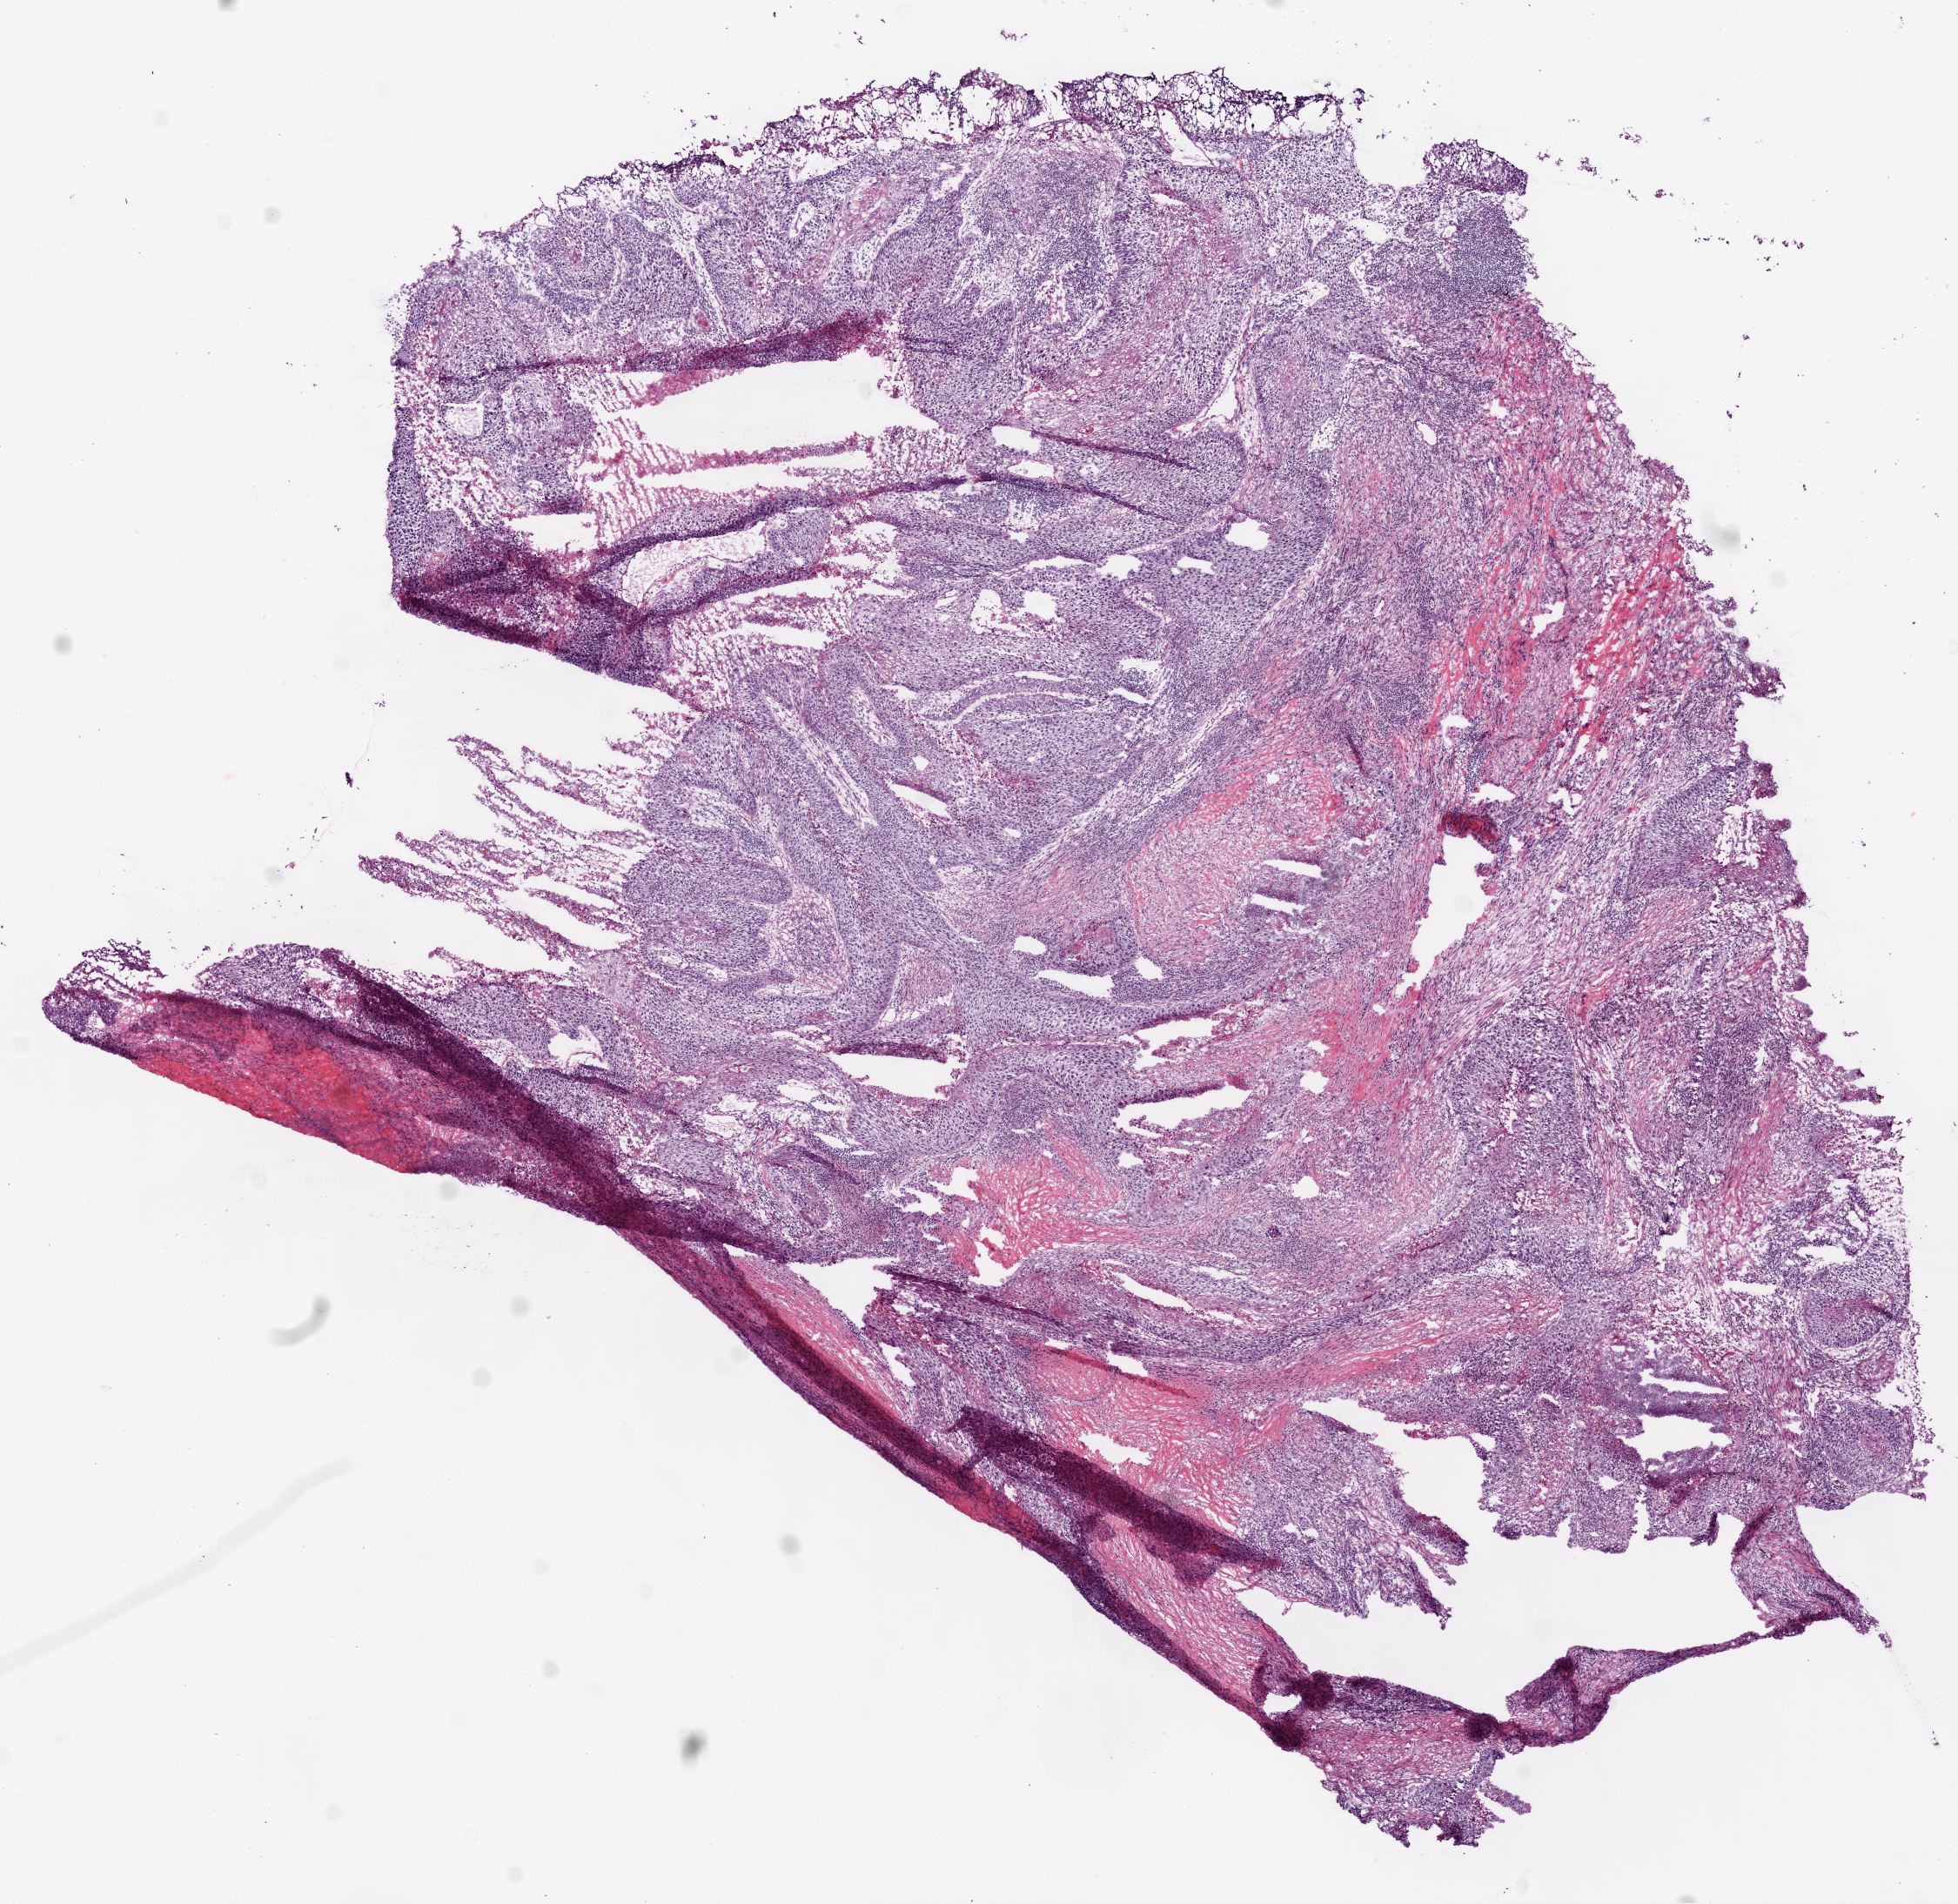
Whole-slide histology image, H&E-stained — whole scanned area (about 9.0 x 8.8 mm, slide scanned at 20x) shown as a low-resolution overview. Frozen section from the bottom of the tissue portion. Sample: primary tumour, lung. Patient: male, age at initial diagnosis 56 years. Slide review estimates, as recorded: tumour cells 74%, tumour nuclei 70%, normal cells 1%, stromal cells 15%, necrosis 10%.
Diagnosis: Squamous cell carcinoma, NOS (lower lobe, lung). AJCC pathologic stage: IB (6th edition). Laterality: left.